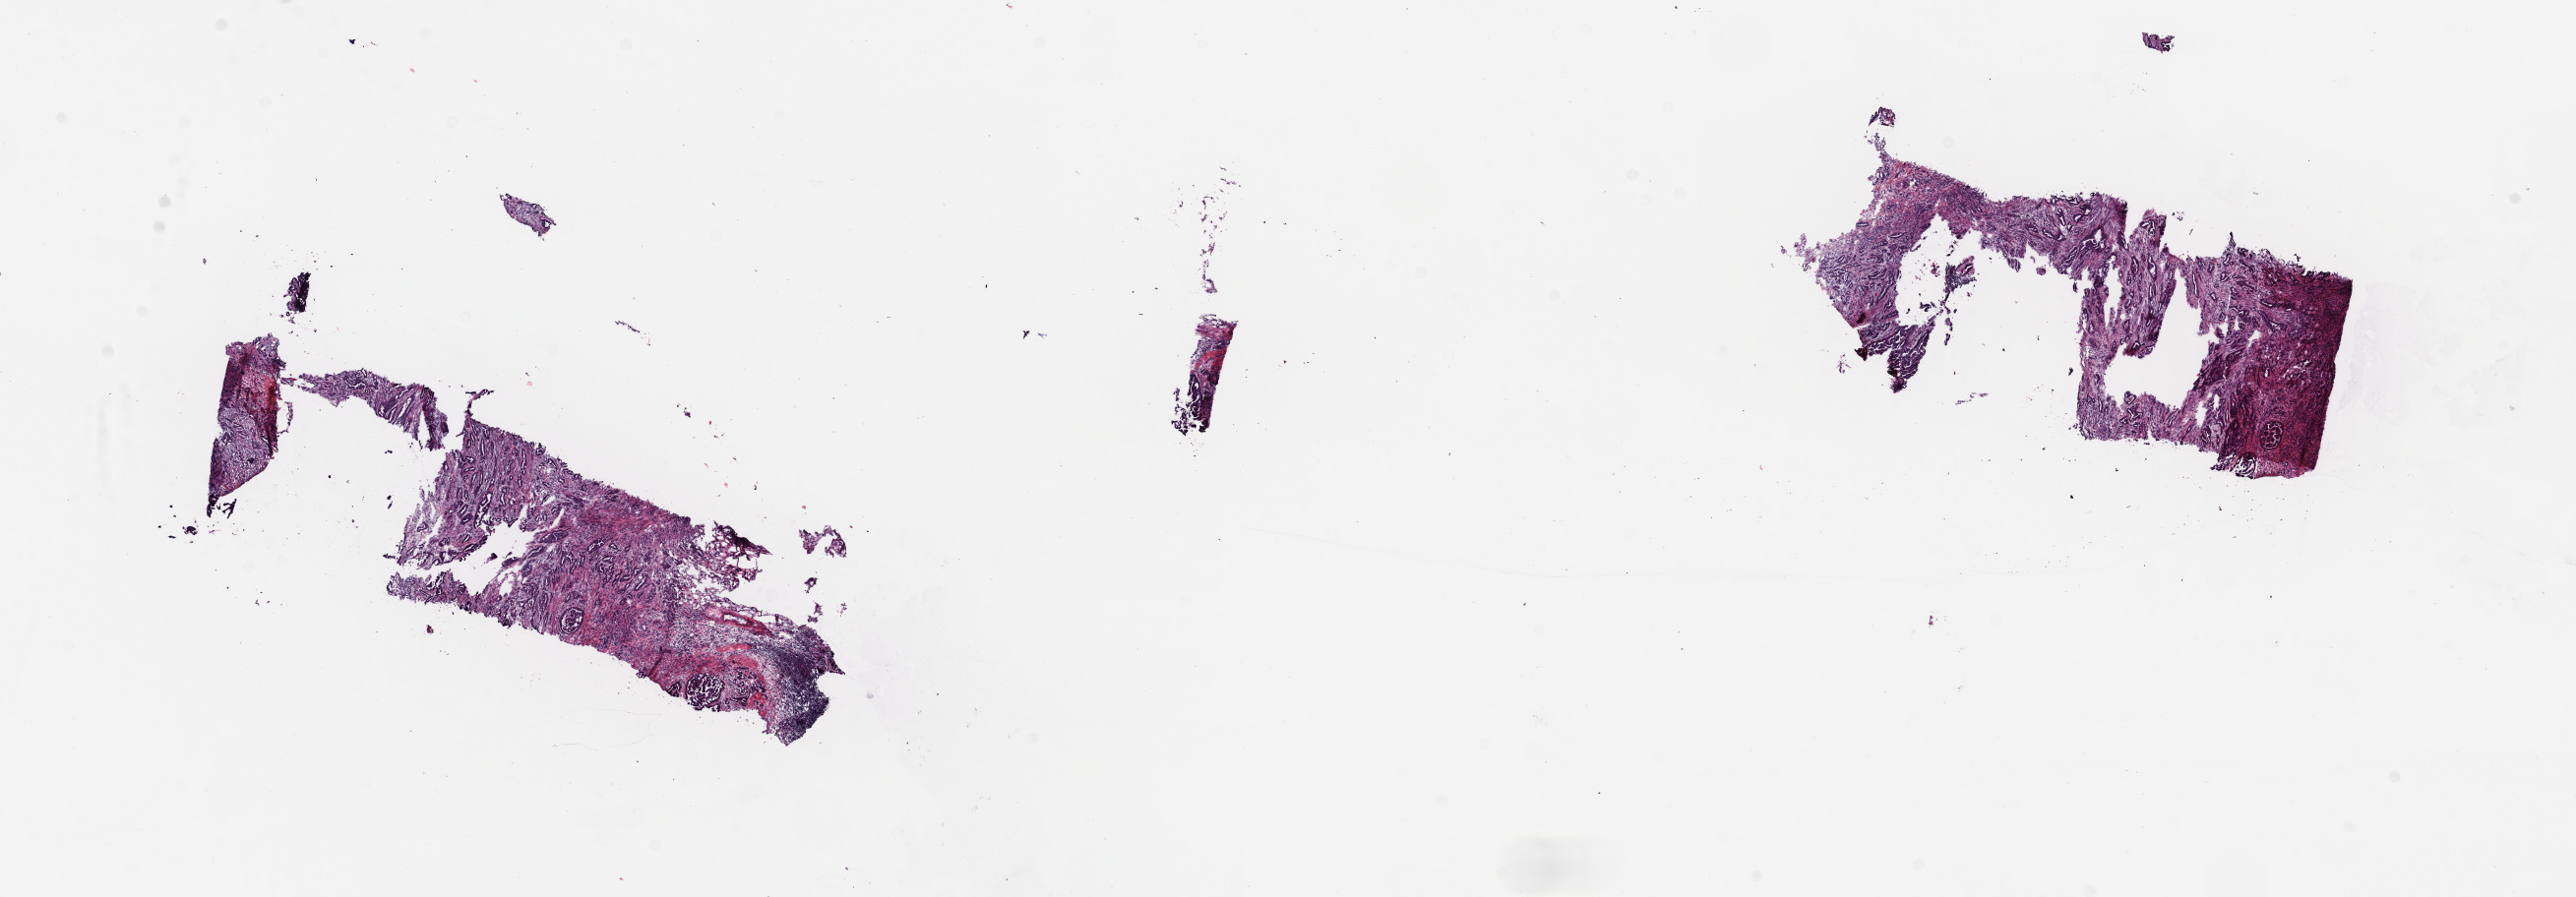
Whole-slide histology image, H&E — shown as a low-resolution overview of the whole scanned area (about 20.7 x 7.2 mm). Frozen section from the top of the tissue portion. Sample: primary tumour, breast. Female patient; age at initial diagnosis 57 years. Composition of this section per pathologist review: tumour cells 50%, tumour nuclei 65%, normal cells 0%, stromal cells 48%, necrosis 2%. Inflammatory infiltration, as recorded: lymphocyte infiltration 5%, monocyte infiltration 0%, neutrophil infiltration 0%.
Diagnosis: Infiltrating duct carcinoma, NOS. Lymph nodes positive (case pathology): 0 of 1 examined. TNM: T1c N0 M0. AJCC pathologic stage: IA (7th edition).